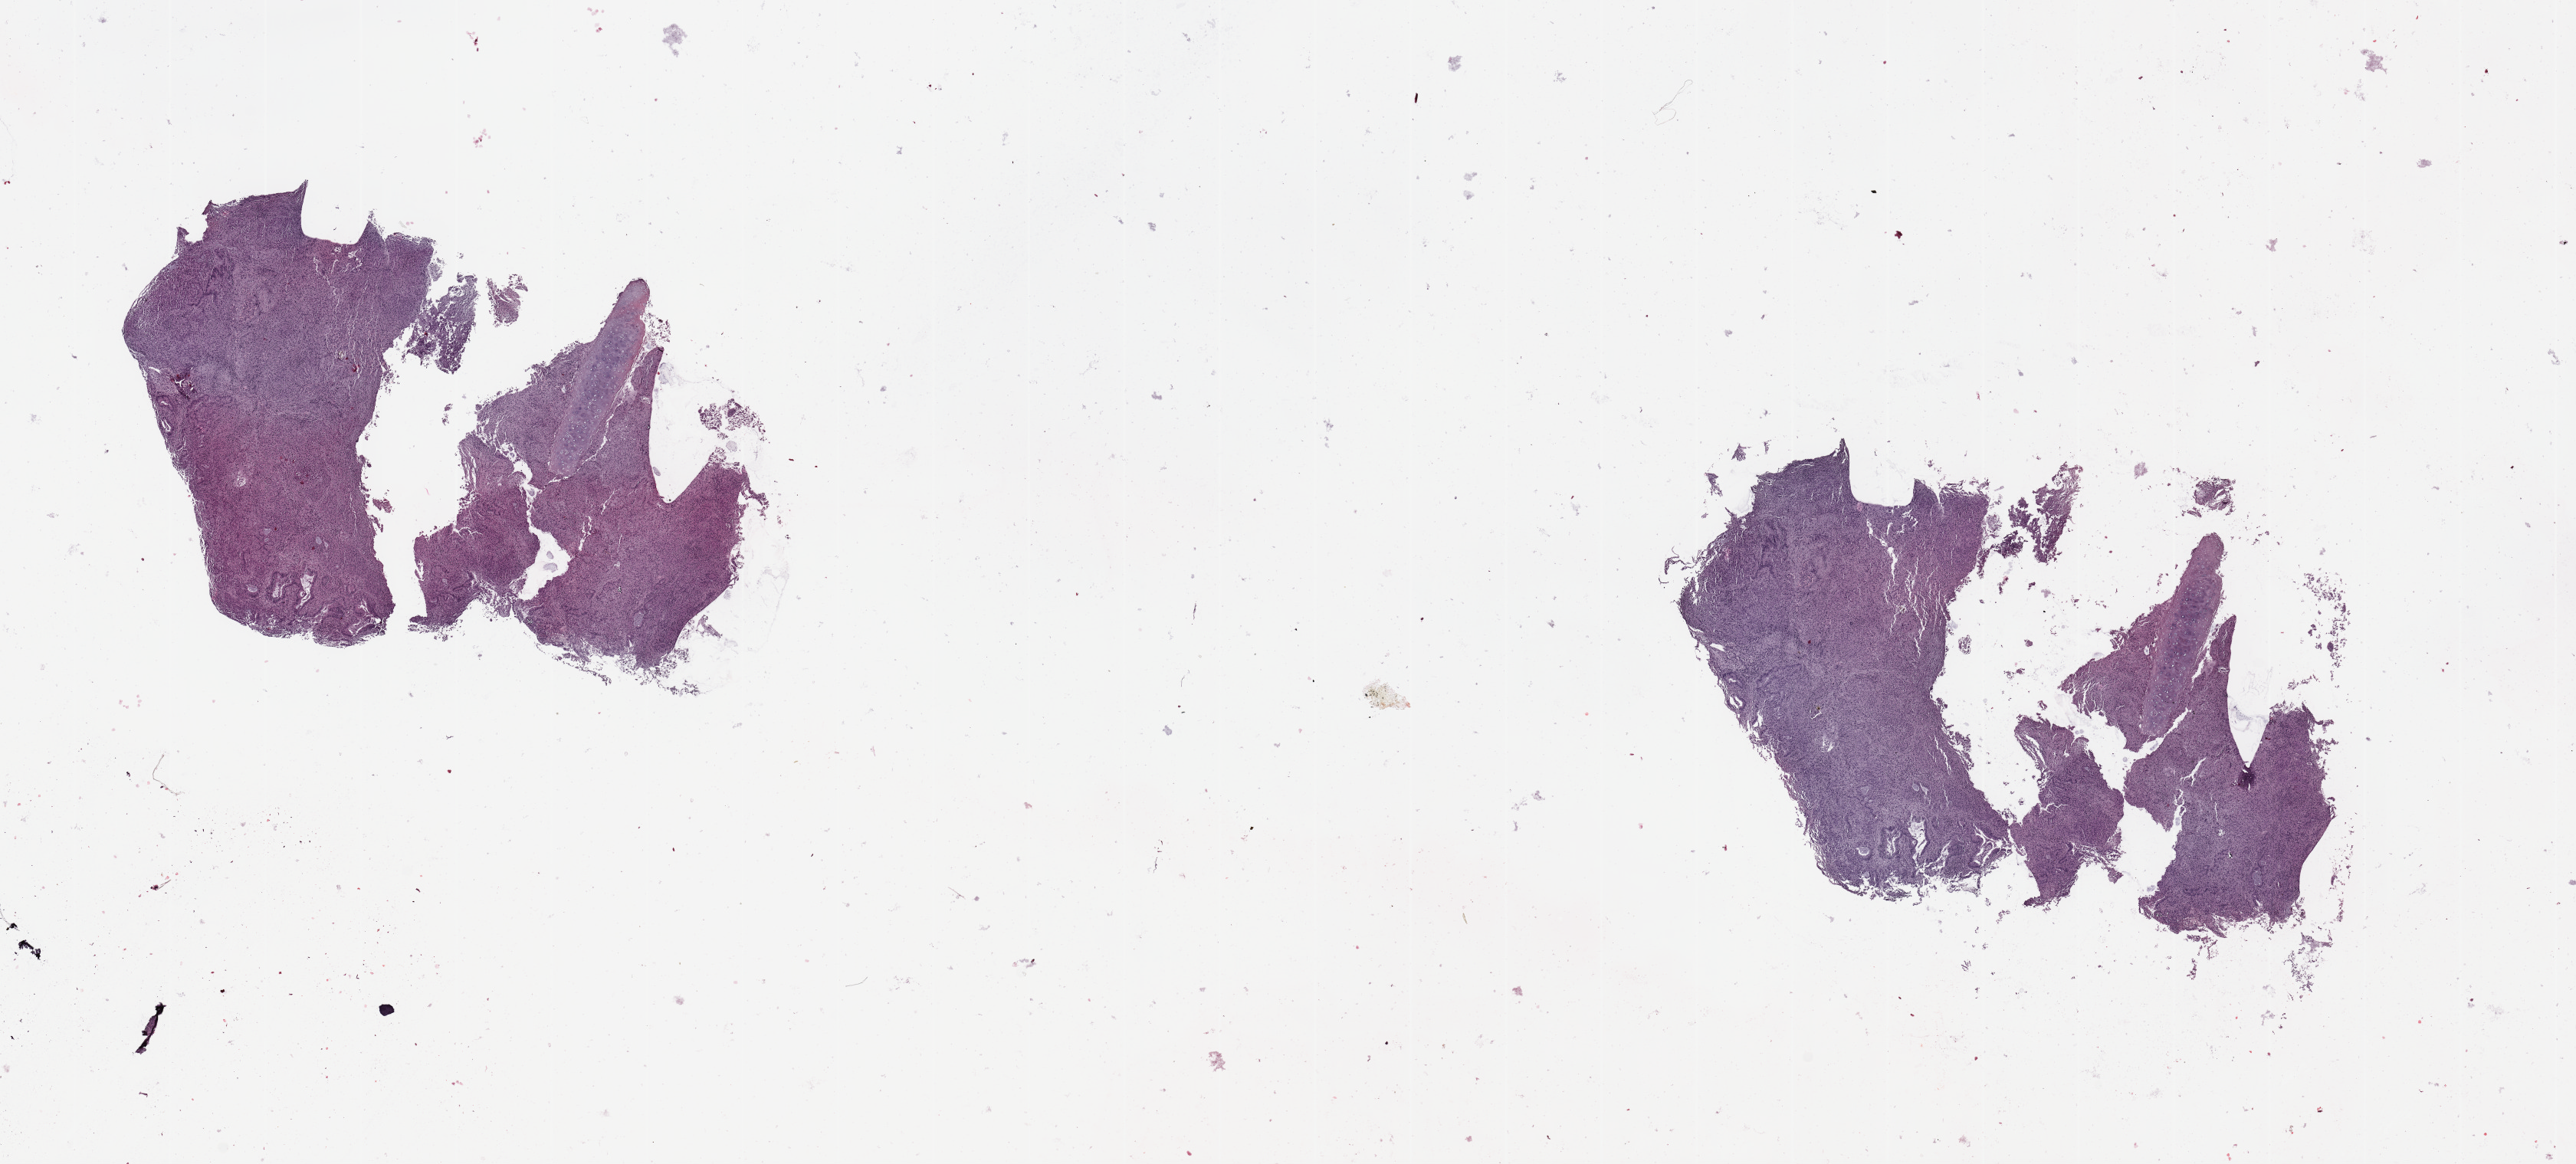
H&E-stained whole-slide image — shown as a low-resolution overview of the whole scanned area (about 26.6 x 12.0 mm, slide scanned at 20x); tumour tissue sample, sampled site: lung. 55-year-old male patient. Histologic grade: G3 (poorly differentiated). Composition of this section per pathologist review: tumour nuclei 75%, necrosis 3%.
Histologic diagnosis: Adenocarcinoma, NOS. AJCC pathologic stage: IV. Primary tumour site (as recorded): right upper lobe.